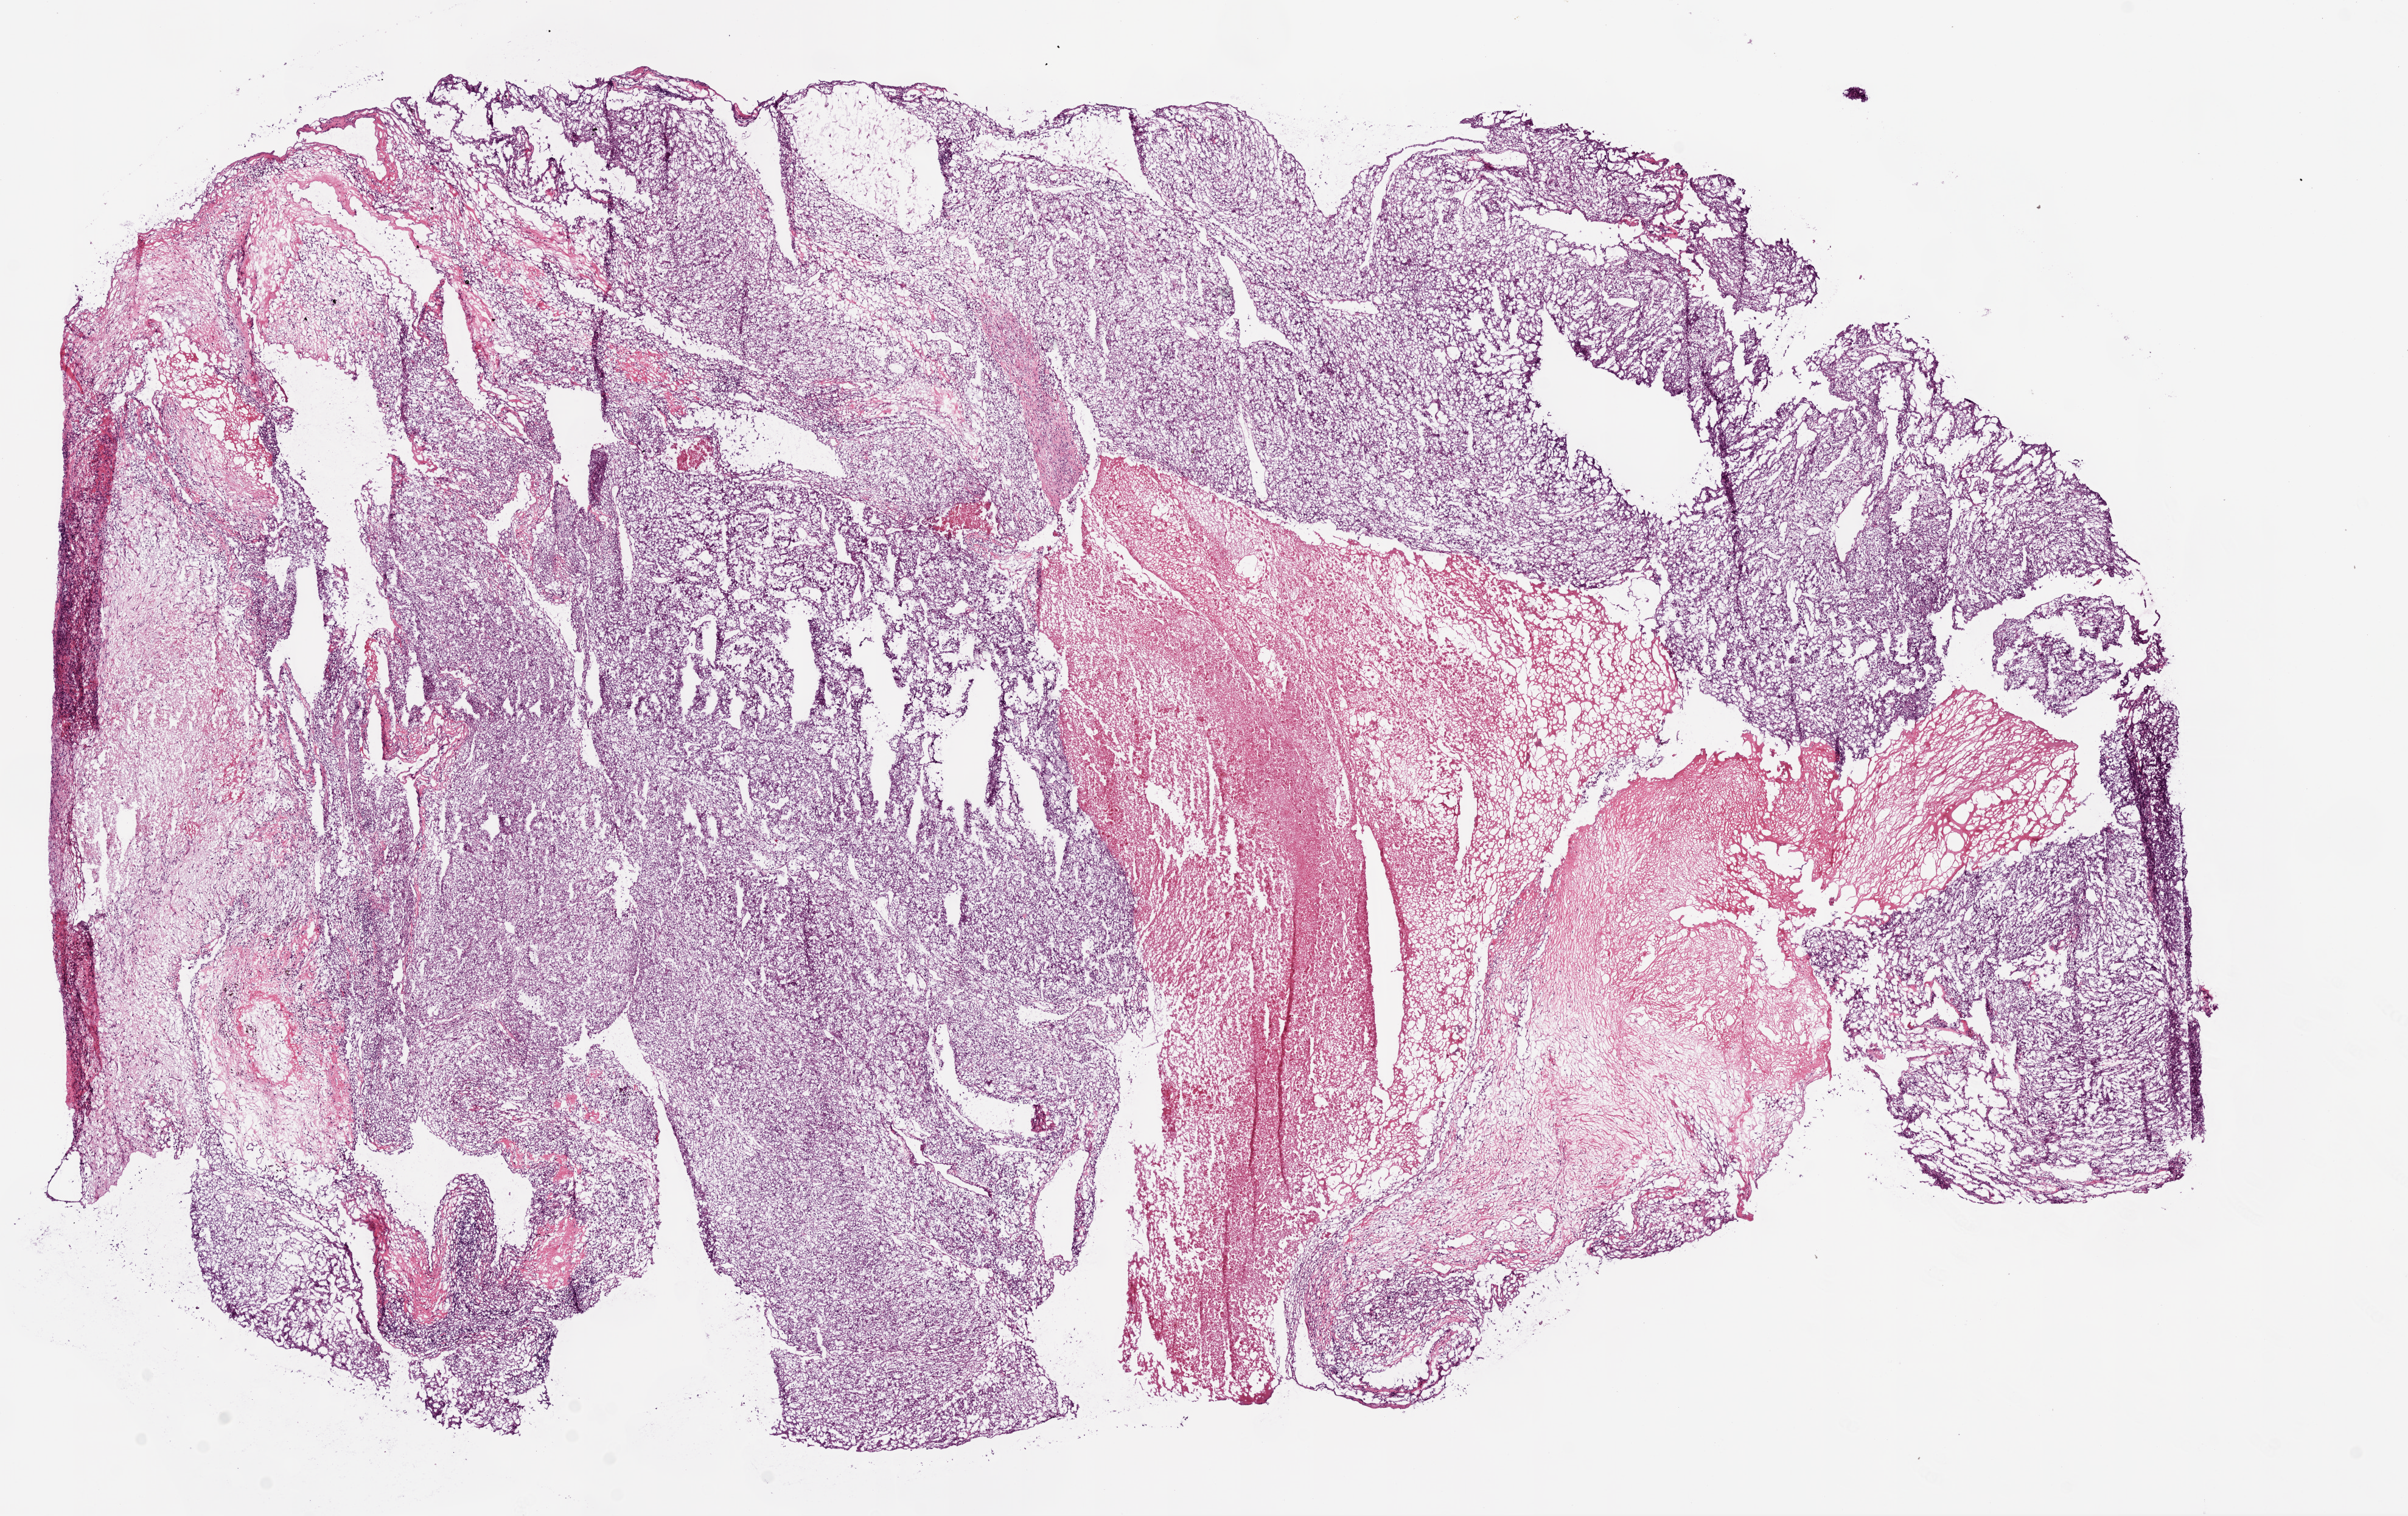
Digitized Hematoxylin and eosin (H&E) stained tissue section (whole slide), whole scanned area (about 16.0 x 10.0 mm, slide scanned at 20x) shown as a low-resolution overview, frozen section from the bottom of the tissue portion, sample: primary tumour, kidney. Female patient; age at initial diagnosis 59 years. Histologic grade: G3 (poorly differentiated). Pathologist review of this section (percent, as recorded): tumour cells 70%, tumour nuclei 85%, normal cells 0%, stromal cells 10%, necrosis 20%.
• diagnosis: Clear cell adenocarcinoma, NOS
• AJCC pathologic stage: I
• TNM: T1b NX M0
• laterality: left